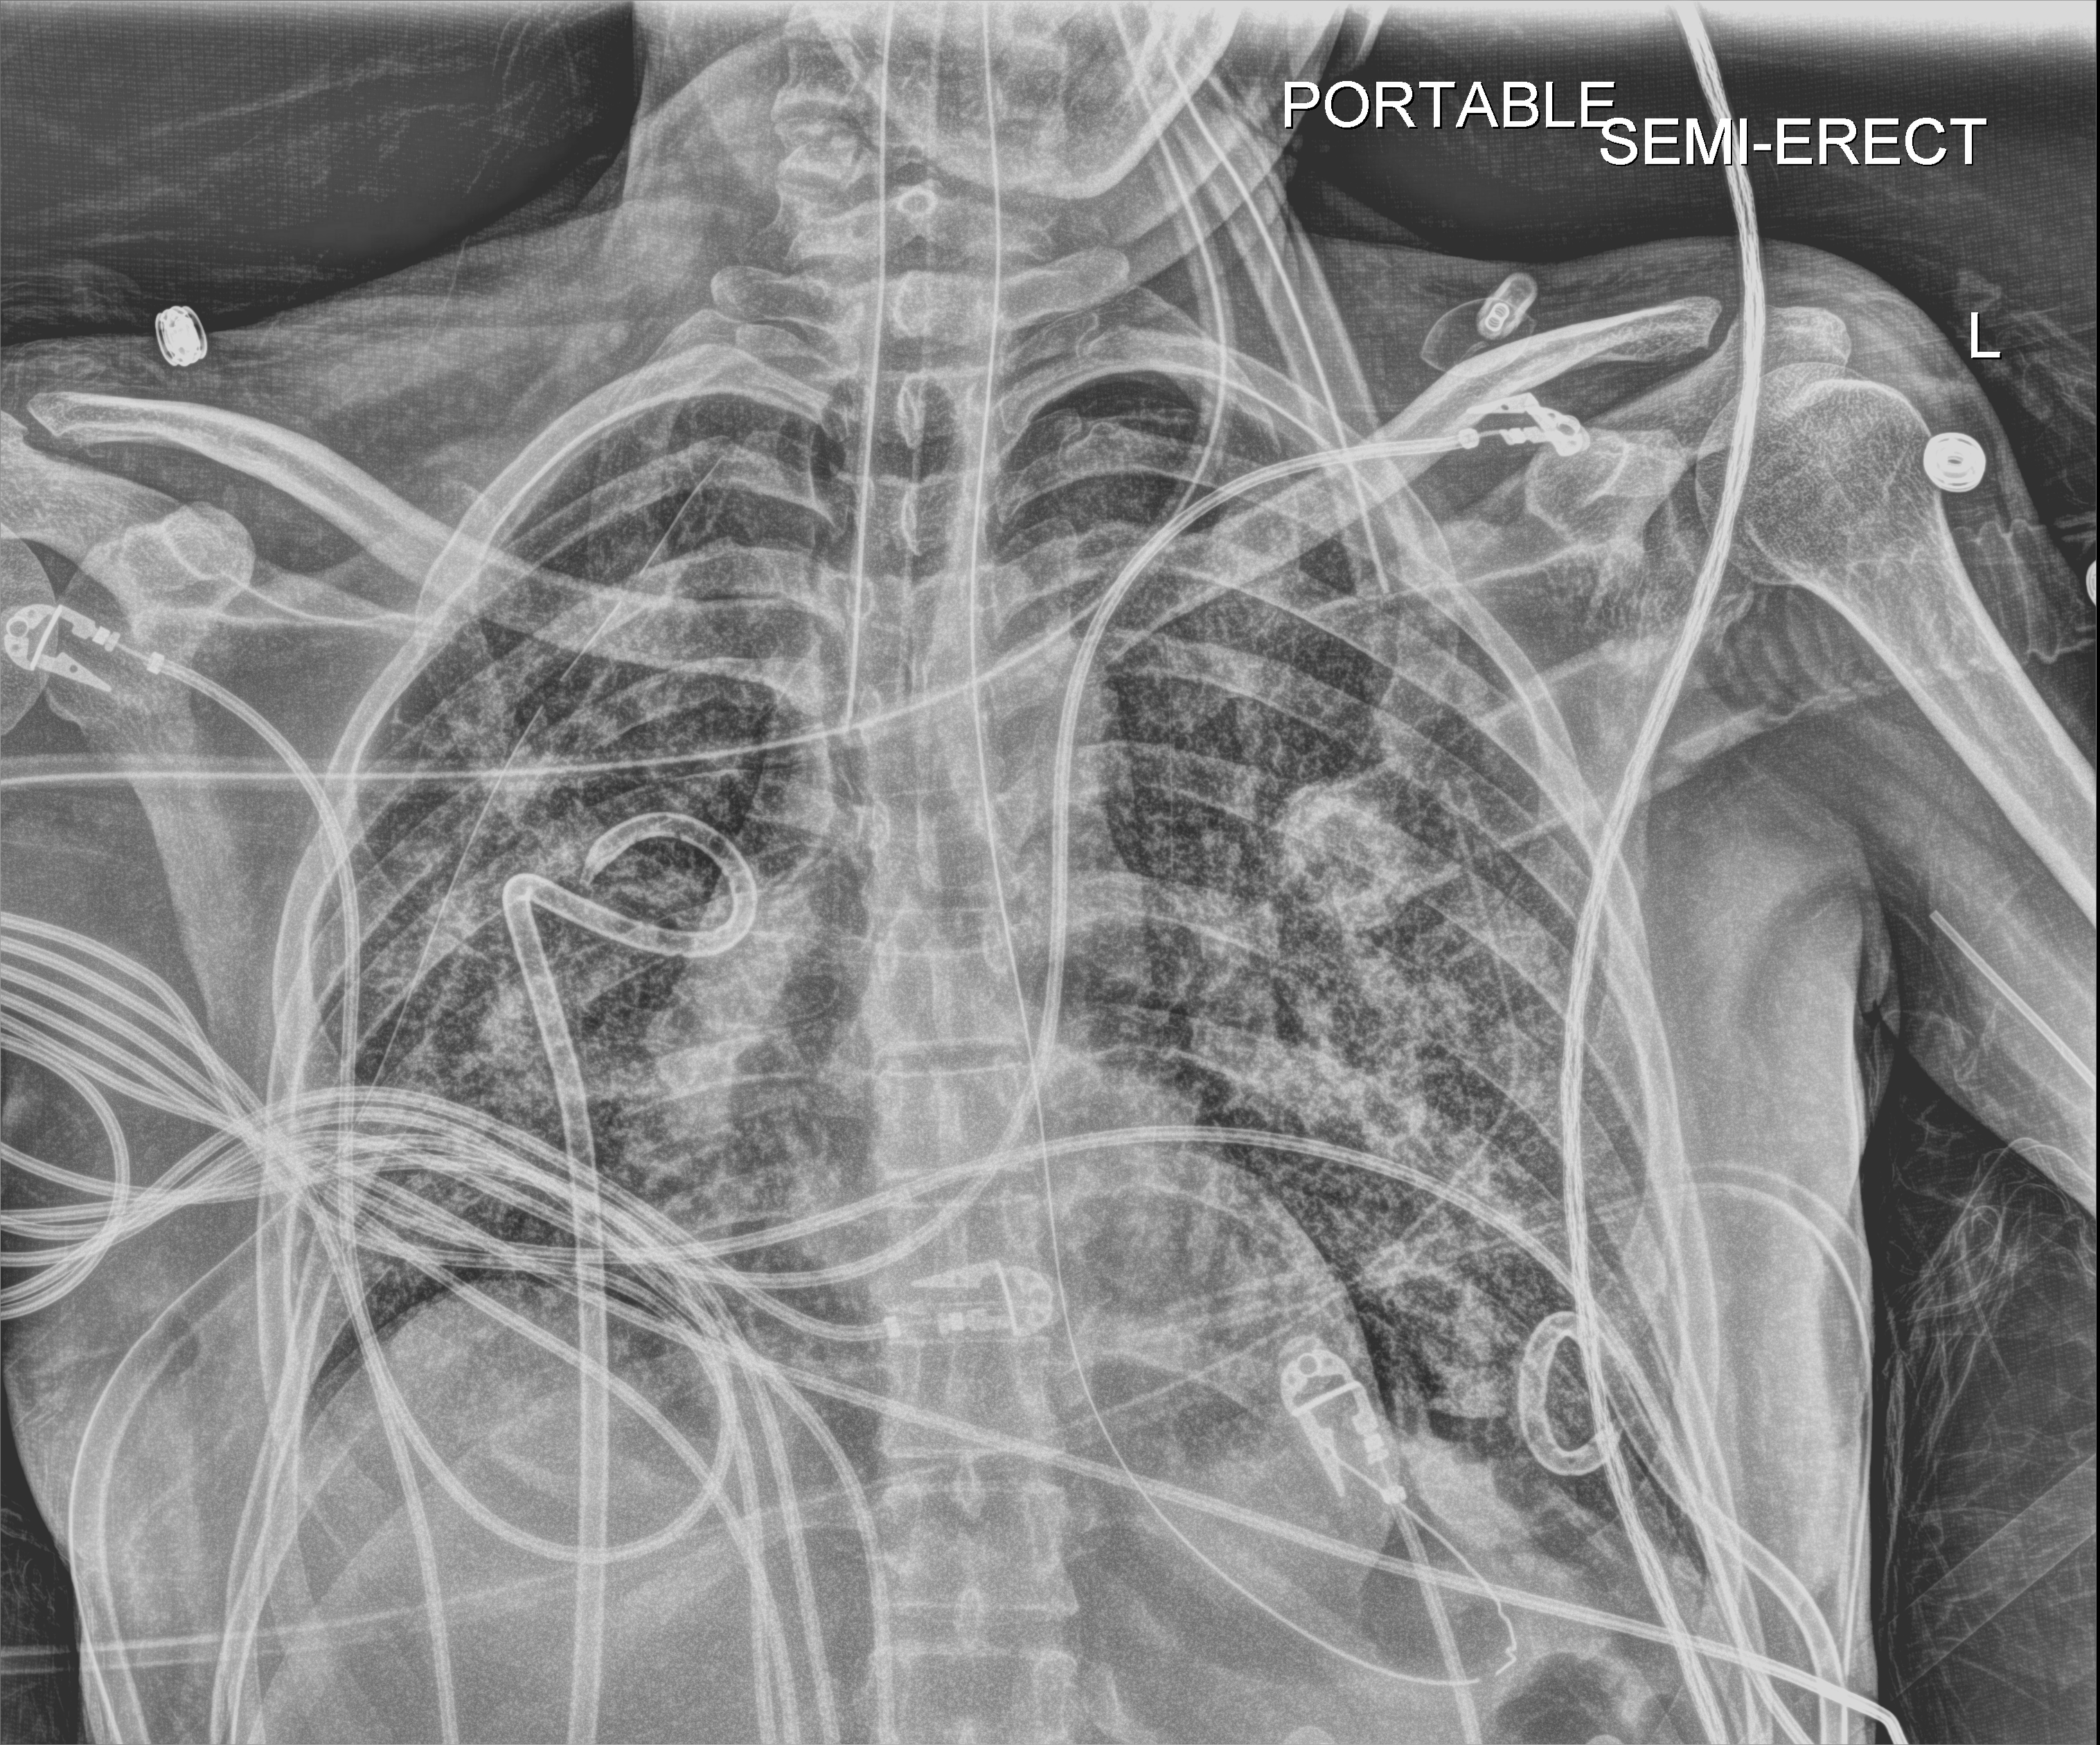
Chest radiograph, anteroposterior (AP) projection. Patient hospitalised with COVID-19, aged 18–59 years.
From the hospital-stay record, not from the radiograph (when in the stay this image was taken is not recorded): other chronic lung disease (admission record): no.